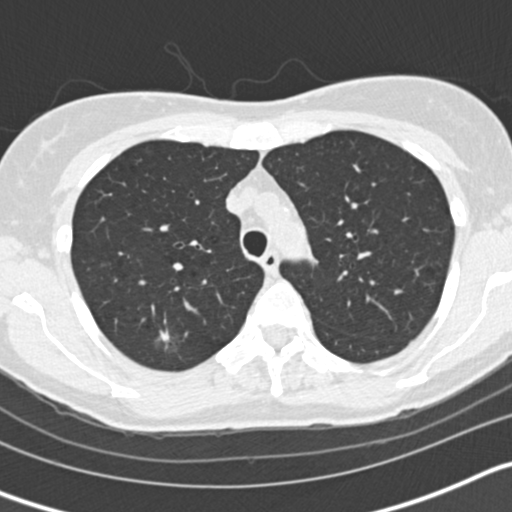
Low-dose screening chest CT, one axial slice. Slice 120 of 163 in the series (ordered by position). Reconstruction kernel B30f. Lung window (W 1500 / L -600 HU). 512 × 512 image matrix, field of view 300 × 300 mm.
Annotated regions visible in this slice (outlined manually by an expert reader):
- lesion 1 (tumor, upper lobe of right lung): bounding box (x1, y1, x2, y2) in pixels: (158, 330, 170, 342)